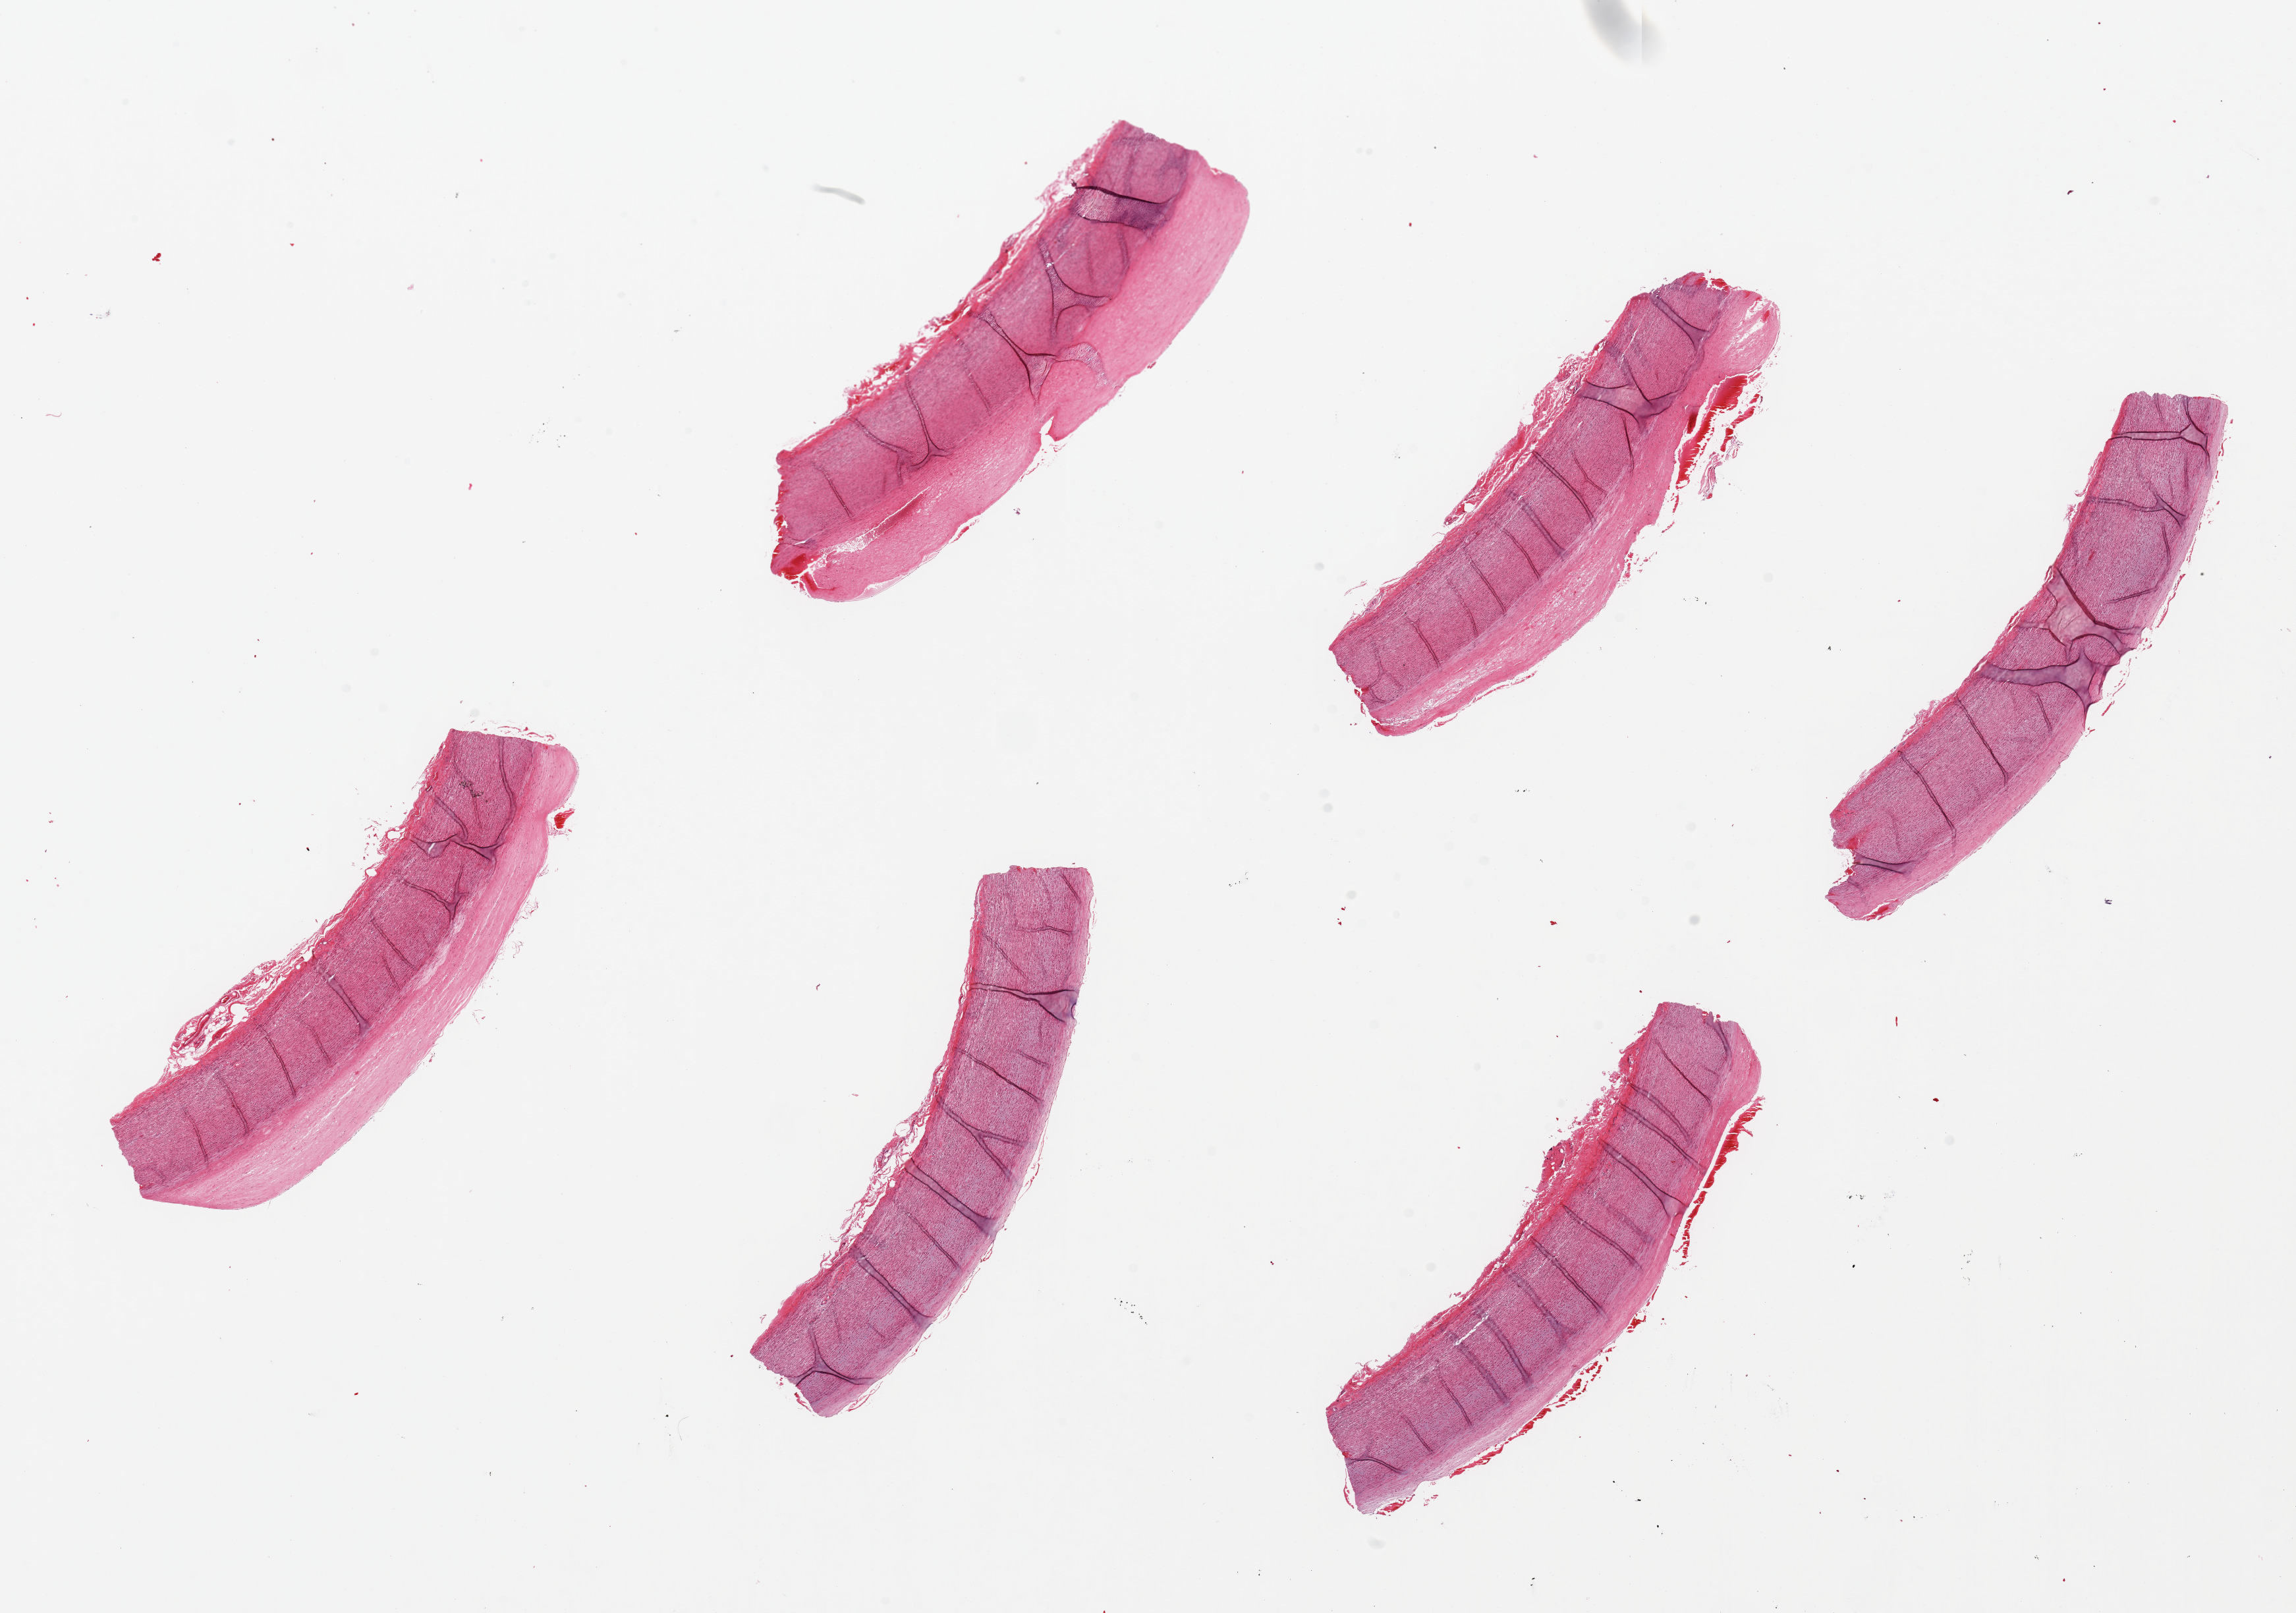
Digitized H&E-stained section, a low-resolution overview of the entire scanned area, about 27.6 x 19.4 mm, PAXgene-fixed paraffin-embedded (PFPE) section, sampled site (target tissue): aorta, tissue donor sample. Donor sex: female.
• pathologist's review note for this sample: 6 pieces, up to 7.5x2mm; atheromatous plaques up to 1 mm thick; well trimmed adventitial fat